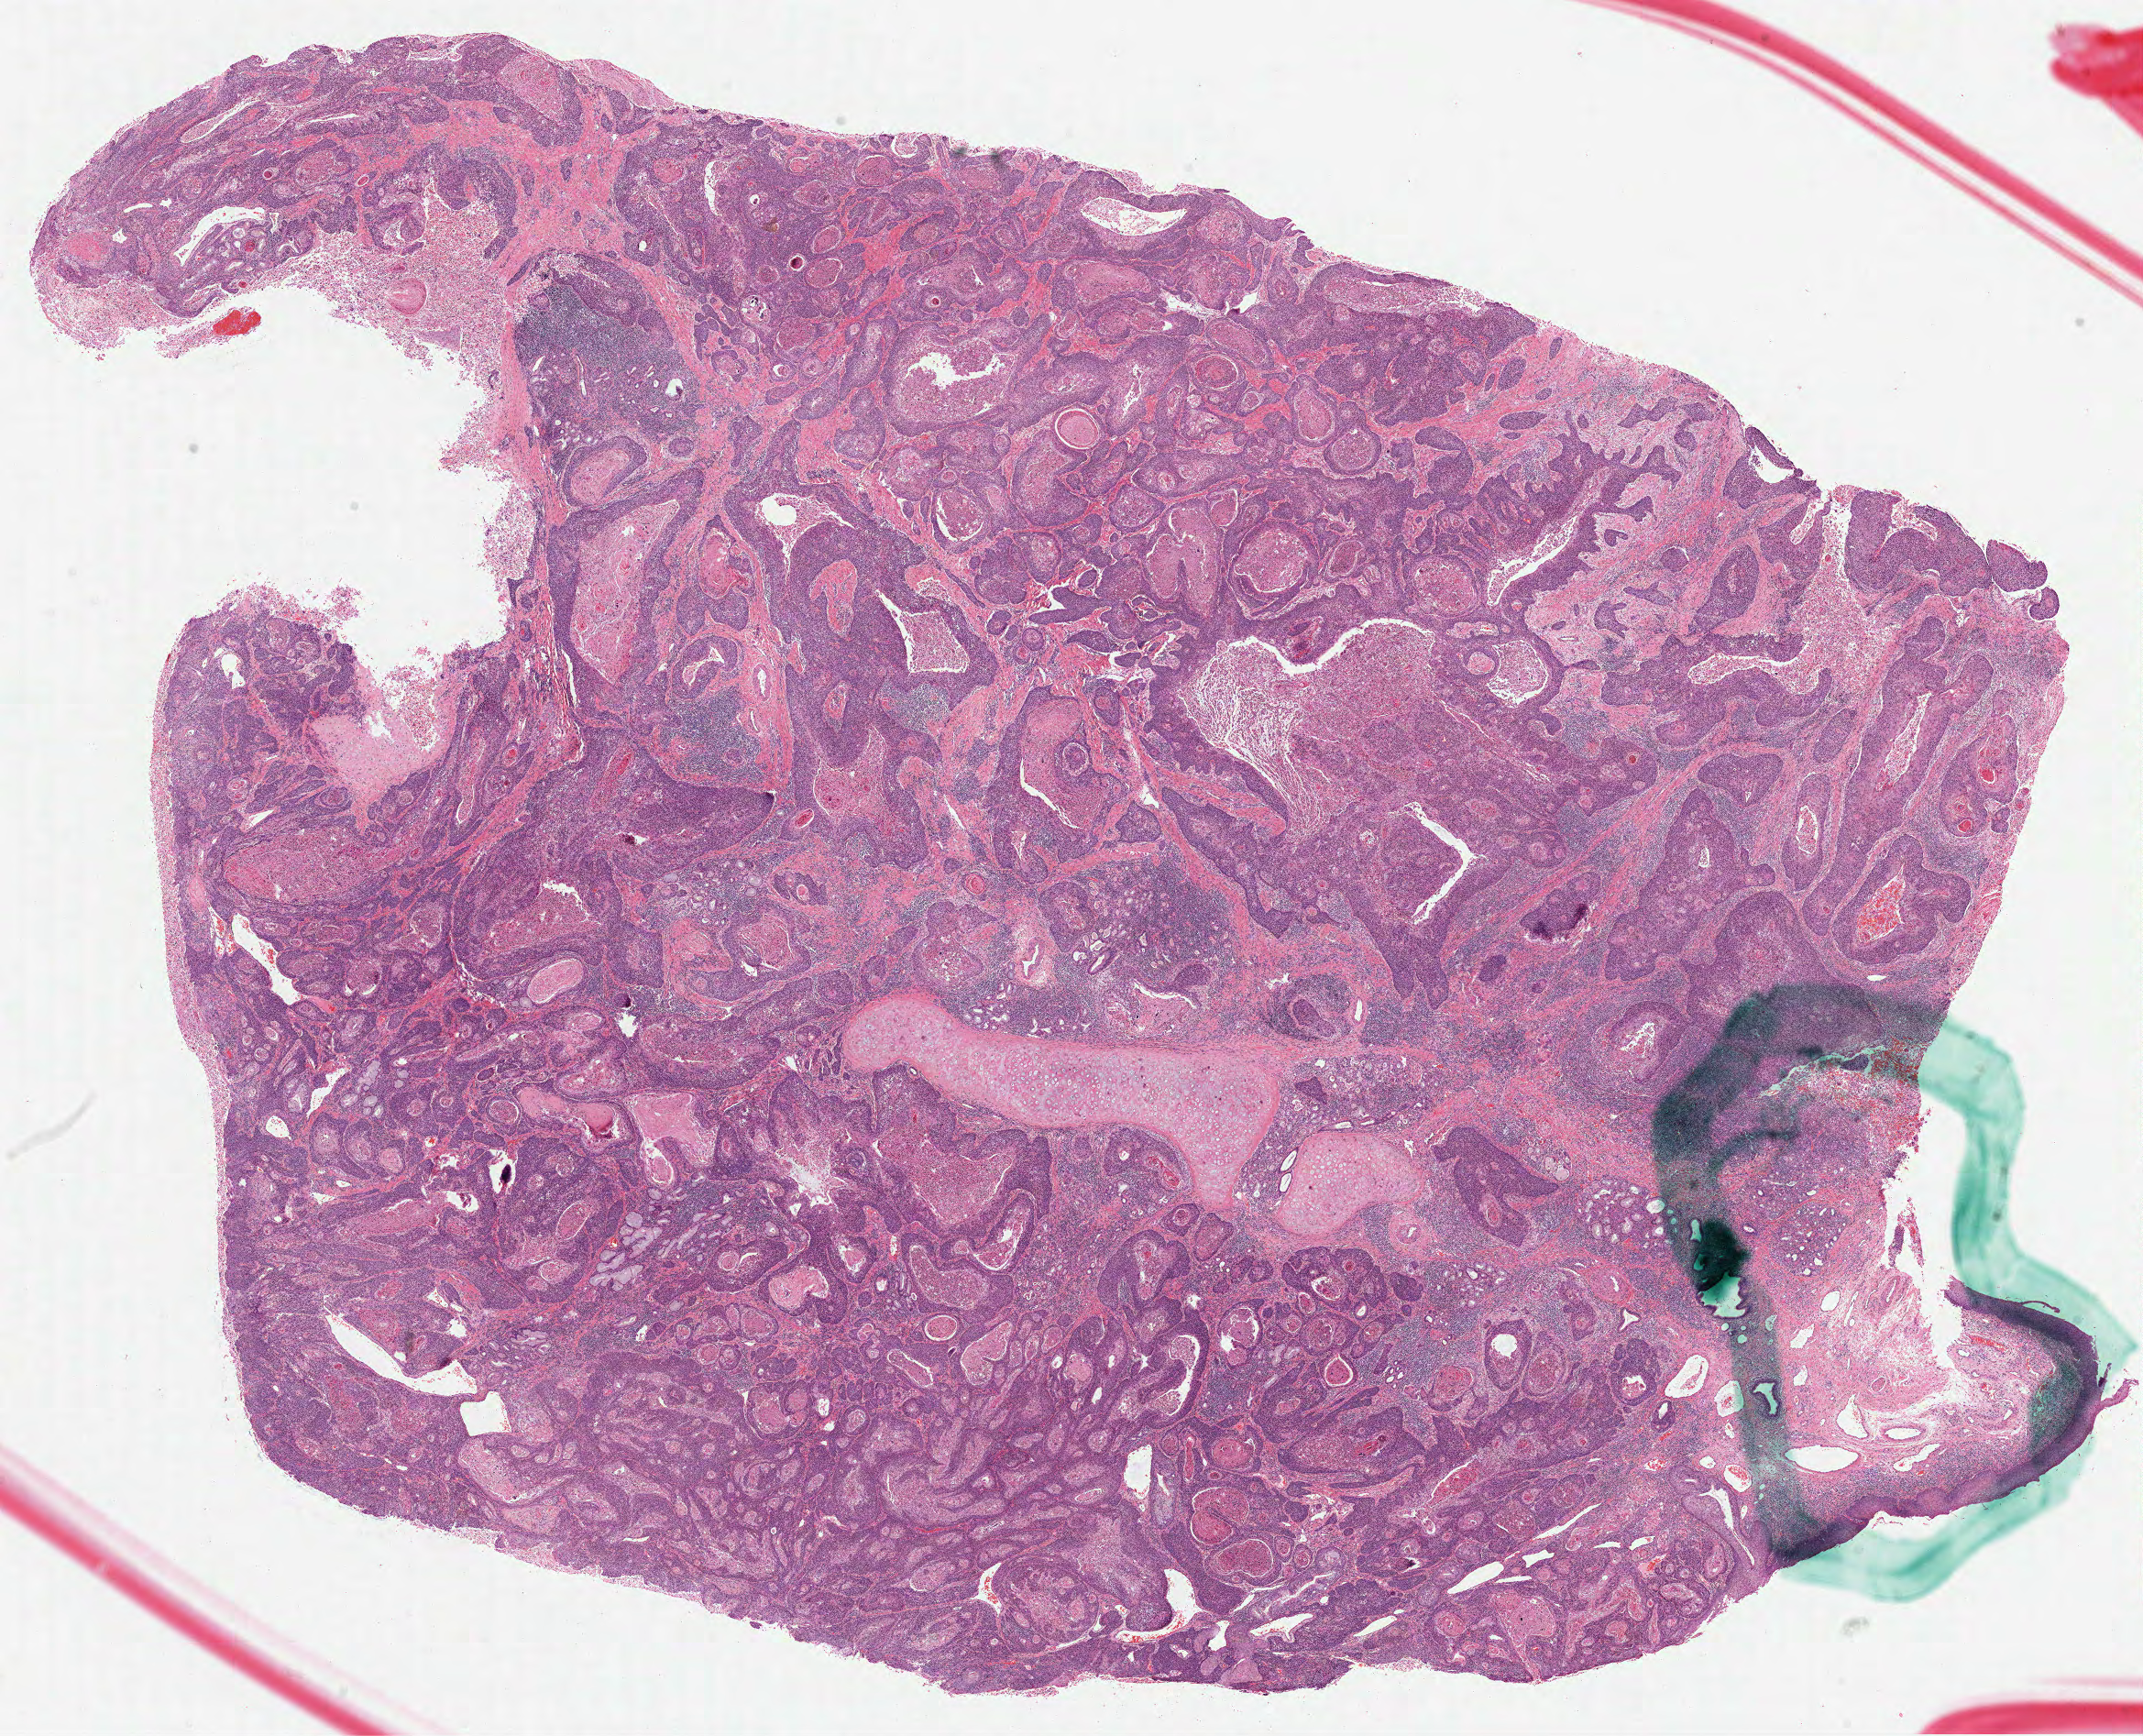
Digitized Hematoxylin and eosin (H&E) stained tissue section (whole slide), shown as a low-resolution overview of the whole scanned area (about 18.9 x 15.3 mm), formalin-fixed paraffin-embedded (FFPE) diagnostic section, sample: primary tumour, head and neck. Male patient; age at initial diagnosis 47 years. Histologic grade: G2 (moderately differentiated).
Histologic diagnosis: Squamous cell carcinoma, NOS. Laterality: left. AJCC pathologic stage: IVA (7th edition).